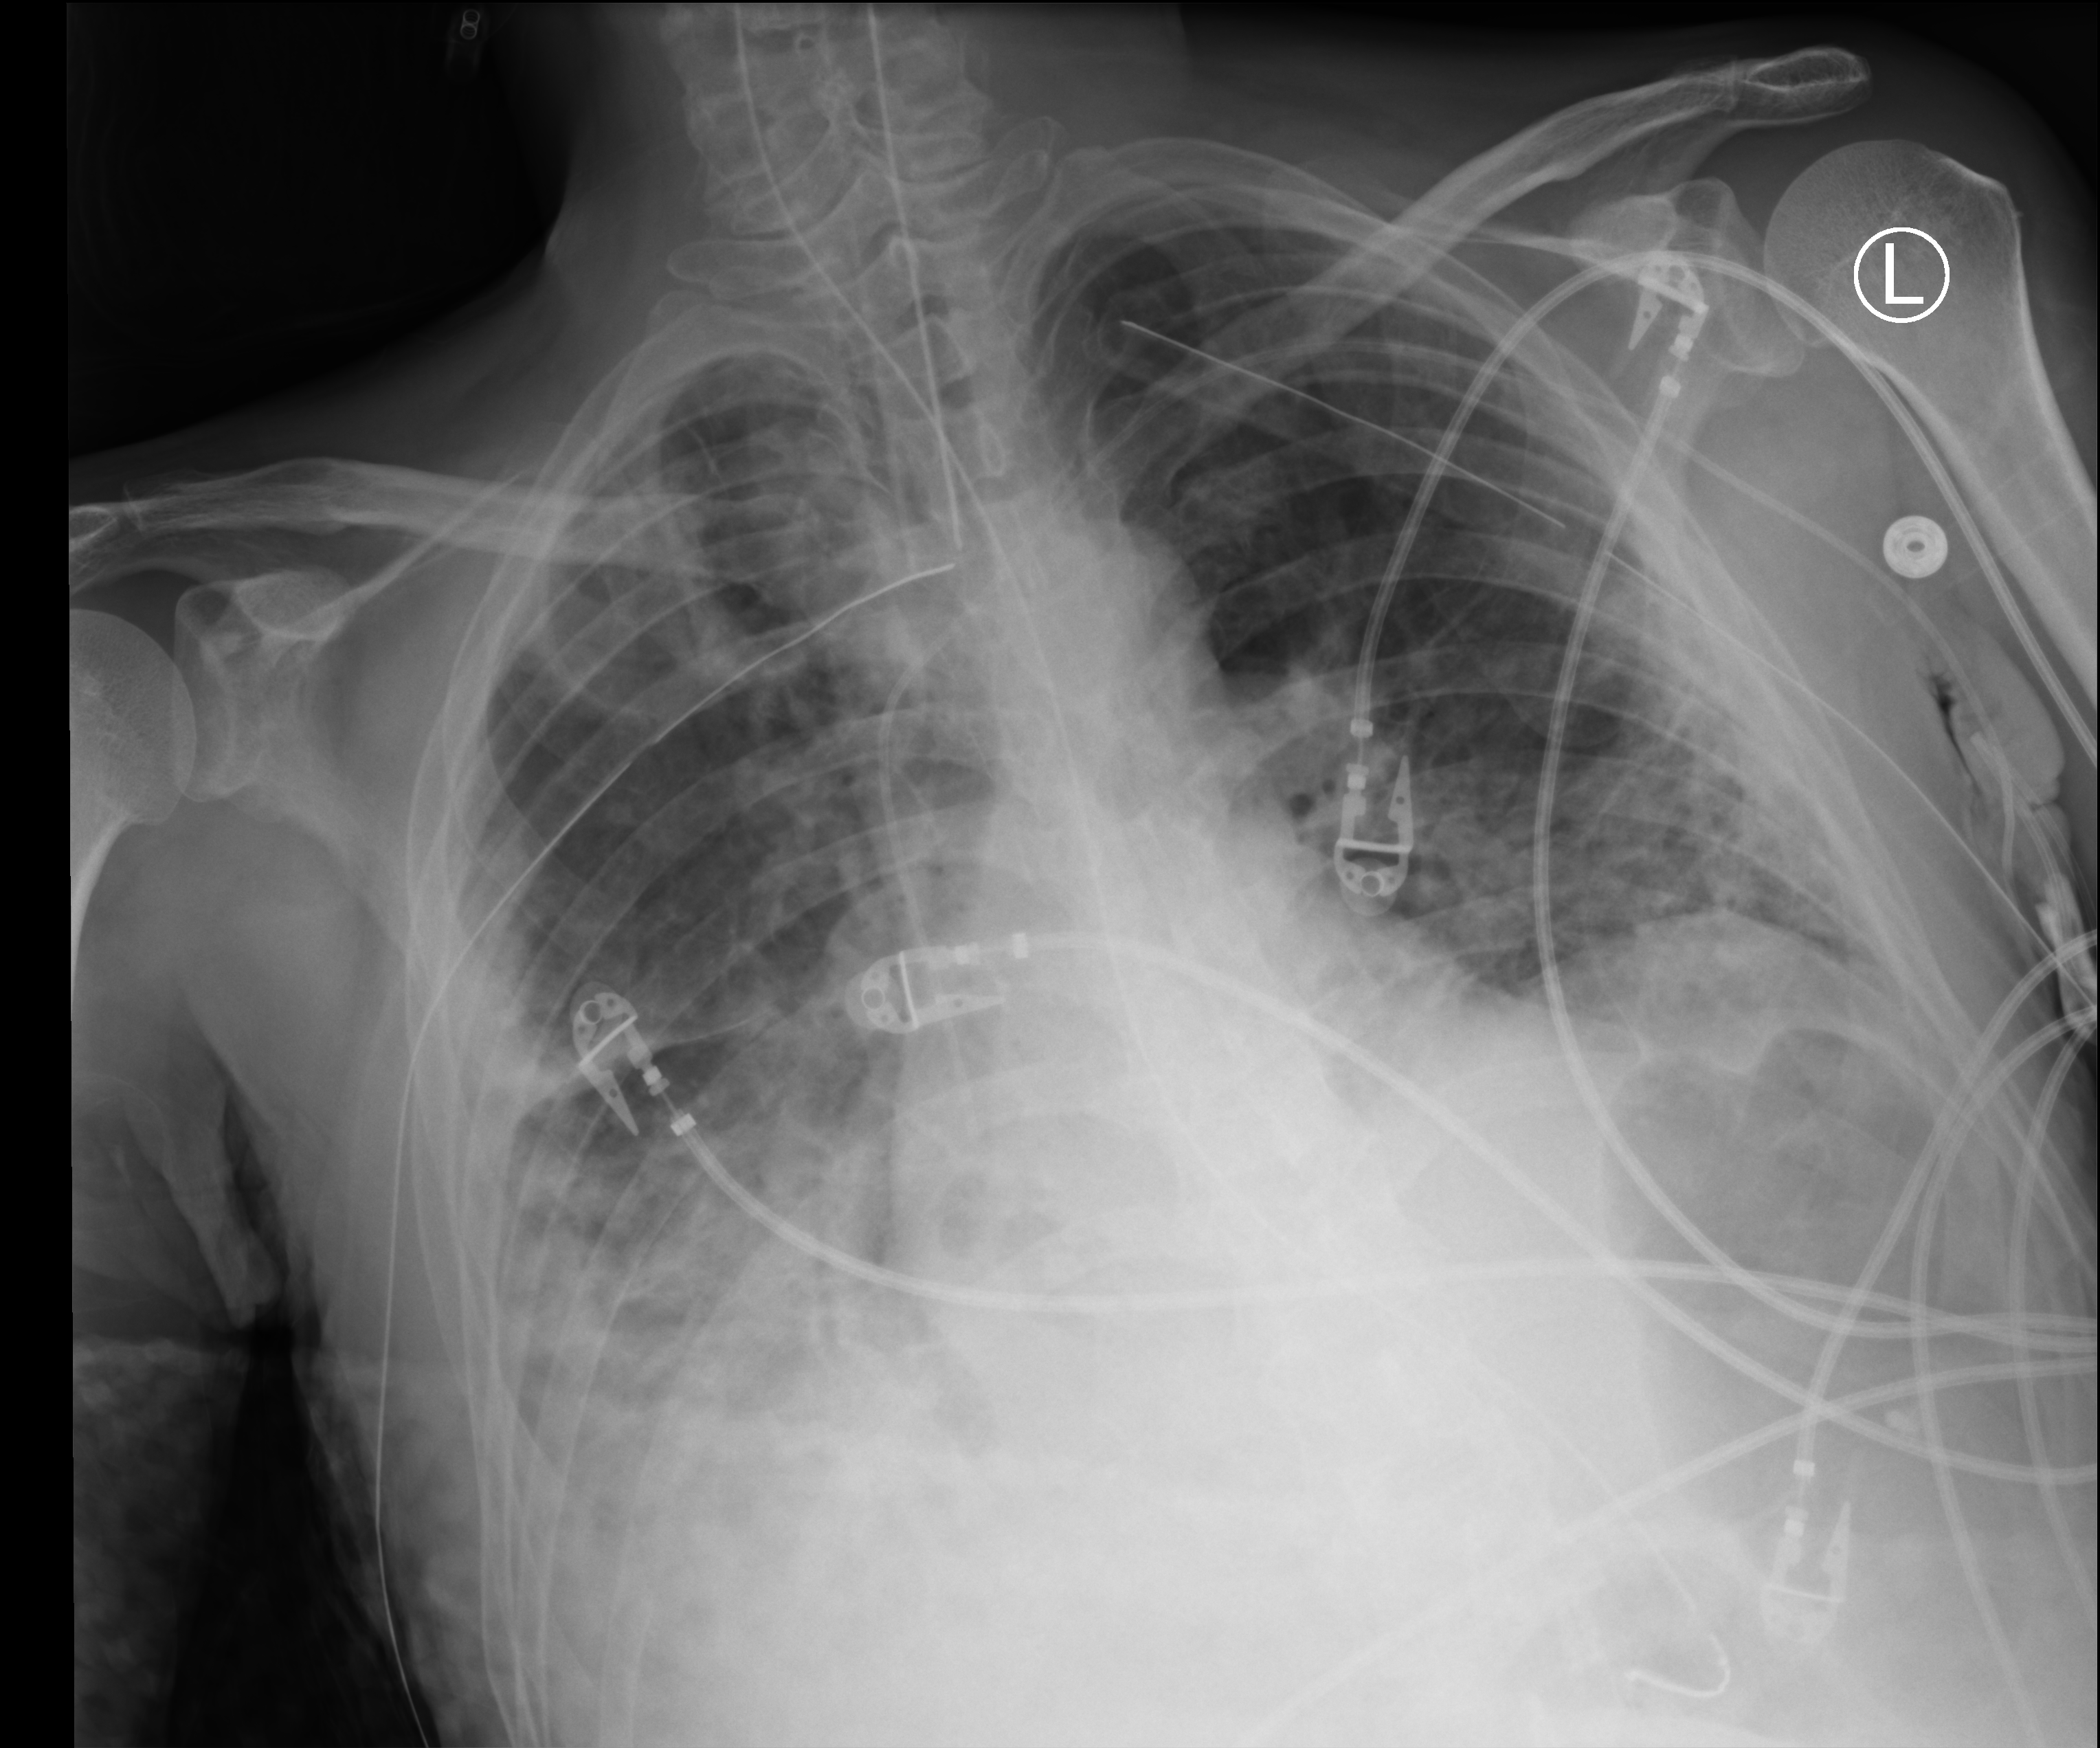
Portable chest radiograph; anteroposterior (AP) projection. Male patient hospitalised with COVID-19, age 18–59 years.
Admission-level facts for this patient (not findings on this image; timing relative to this image not recorded):
- hypertension (admission record): yes